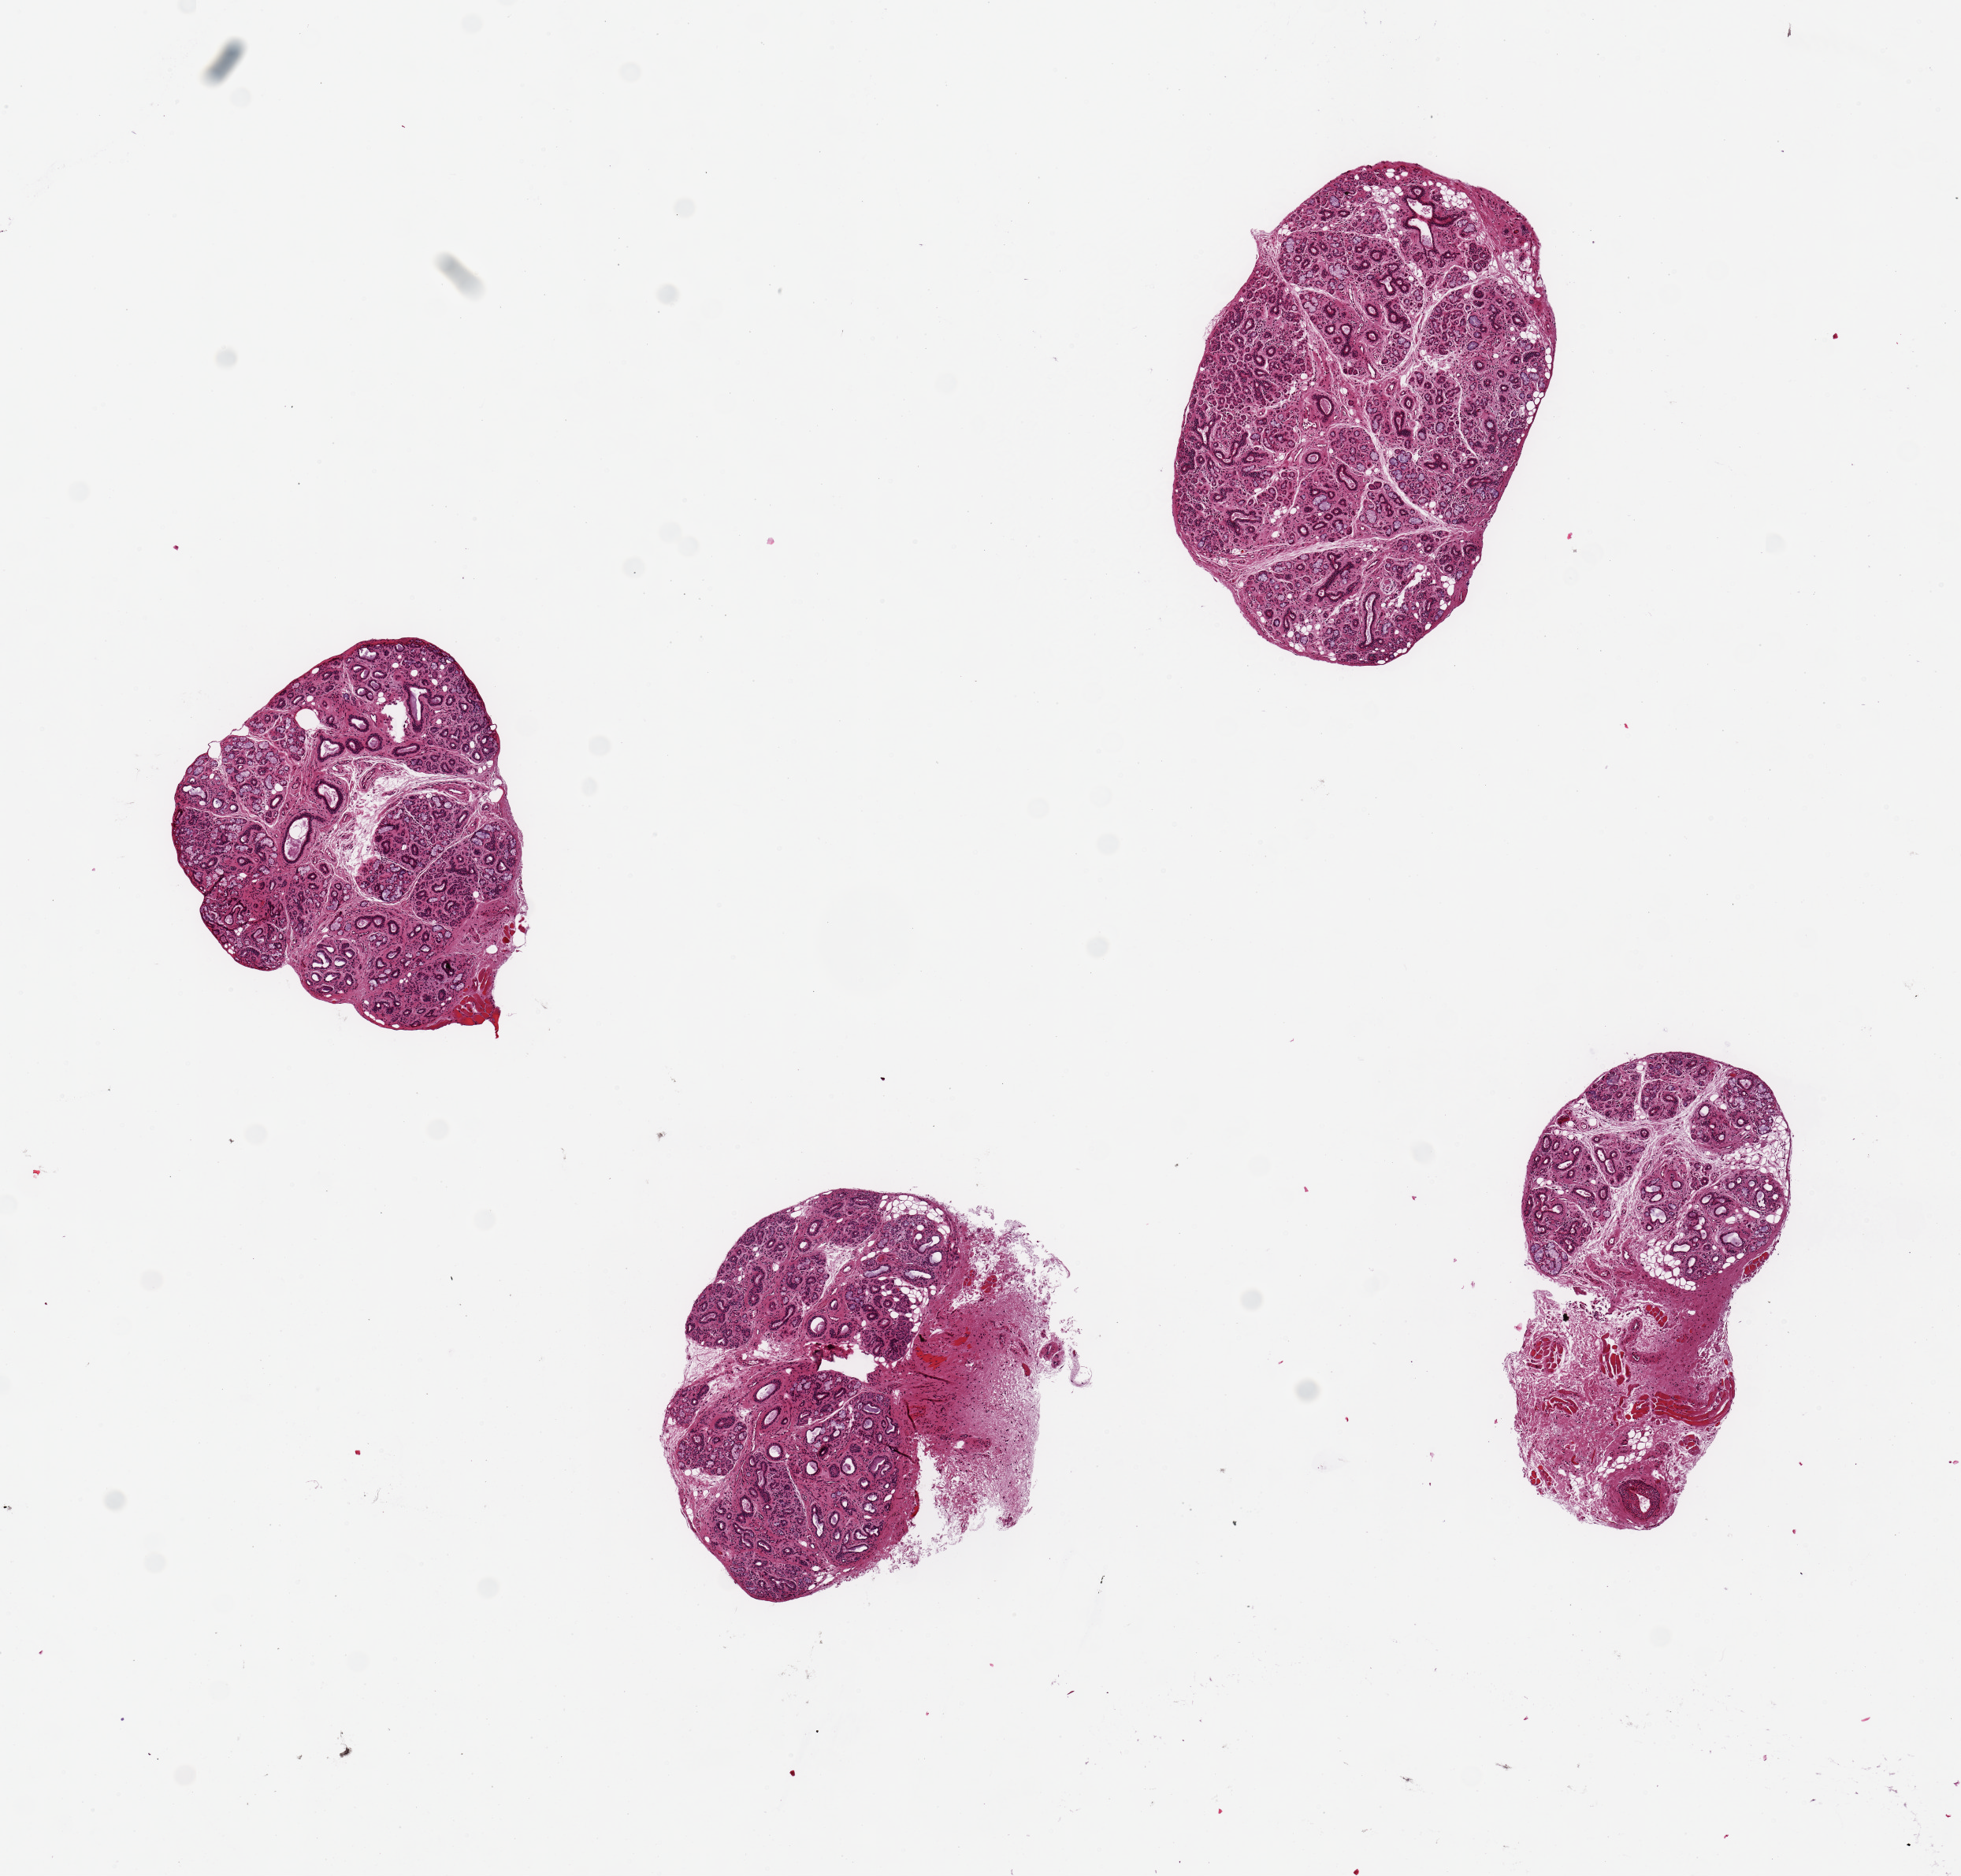
Hematoxylin and eosin (H&E) whole-slide image — a low-resolution overview of the entire scanned area, about 9.8 x 9.4 mm. PAXgene-fixed paraffin-embedded (PFPE) section. Section of minor salivary gland (target tissue). Tissue donor sample. Donor: female.
- pathologist's review note for this sample: 4 pieces, up to 2x2mm; excellent specimens, well preserved, 2 of 4 have ~40% fat/fibrous tissue